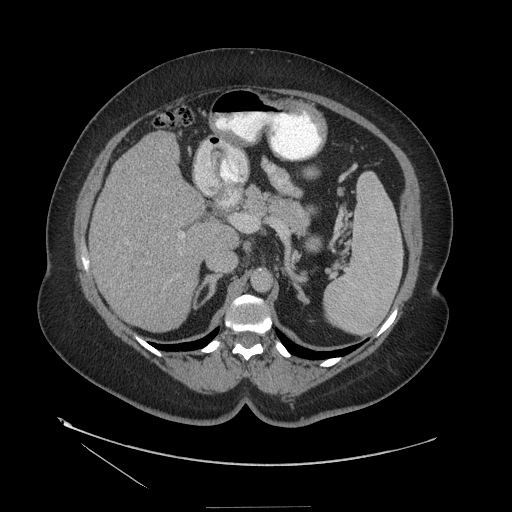
Contrast-enhanced abdominal CT (liver protocol), one axial slice; position 70 of 127 along the scan axis; 140 kVp; soft-tissue window (W 400 / L 40 HU); 512 × 512 image matrix, field of view 480 × 480 mm. Case-level facts recorded for this patient, not image findings: diagnosis: hepatocellular carcinoma (patient treated with transarterial chemoembolisation; whether this scan precedes or follows treatment is not stated here); TNM stage (as recorded): Stage-II.
Outlined on this slice (semi-automatically segmented with operator editing):
- liver parenchyma outside the tumour (the mass and vessels are separate outlines, so this box may not span the whole liver): bounding box [x1, y1, x2, y2] px = [90, 132, 204, 332]
- liver vessels: [181, 233, 185, 237]